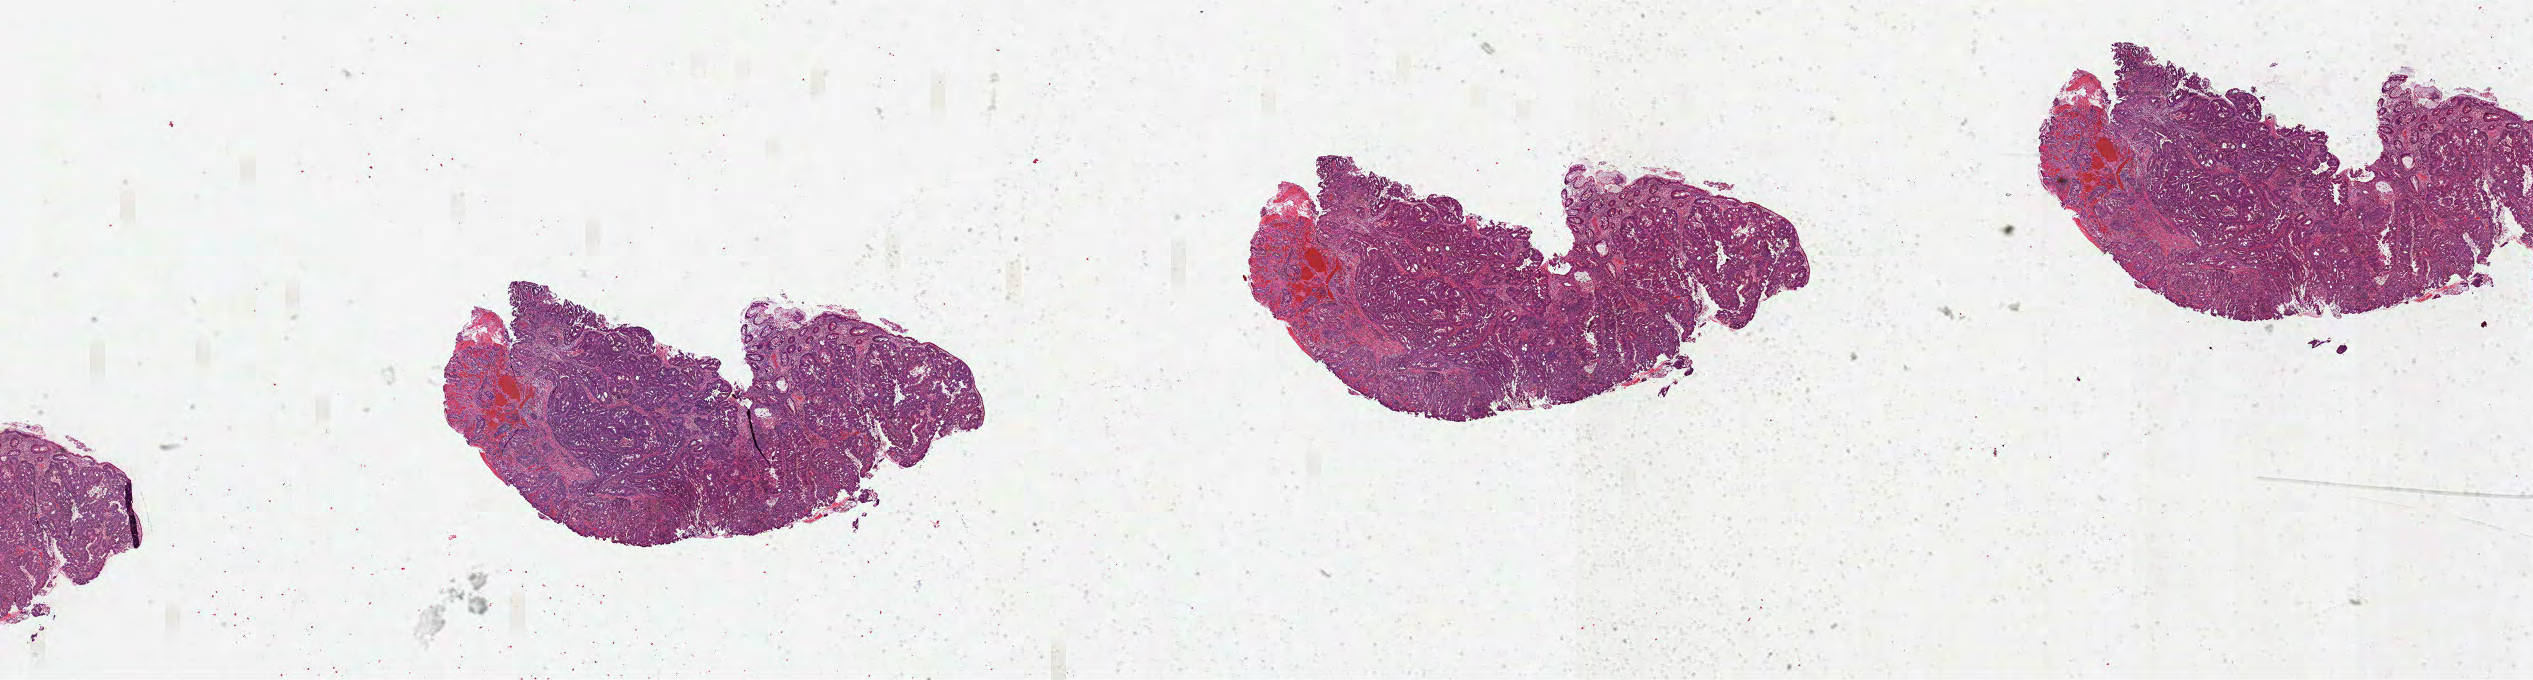
Digitized H&E tissue section (whole slide), a low-resolution overview of the entire scanned area, about 40.9 x 11.0 mm. Formalin-fixed paraffin-embedded (FFPE) diagnostic section. Colon, primary tumour sample. Patient: female, age at initial diagnosis 69 years.
- lymph nodes positive (case pathology): 0 of 19 examined
- TNM: T3 N0 M0
- AJCC pathologic stage: IIA (7th edition)
- diagnosis: Adenocarcinoma, NOS (ascending colon)